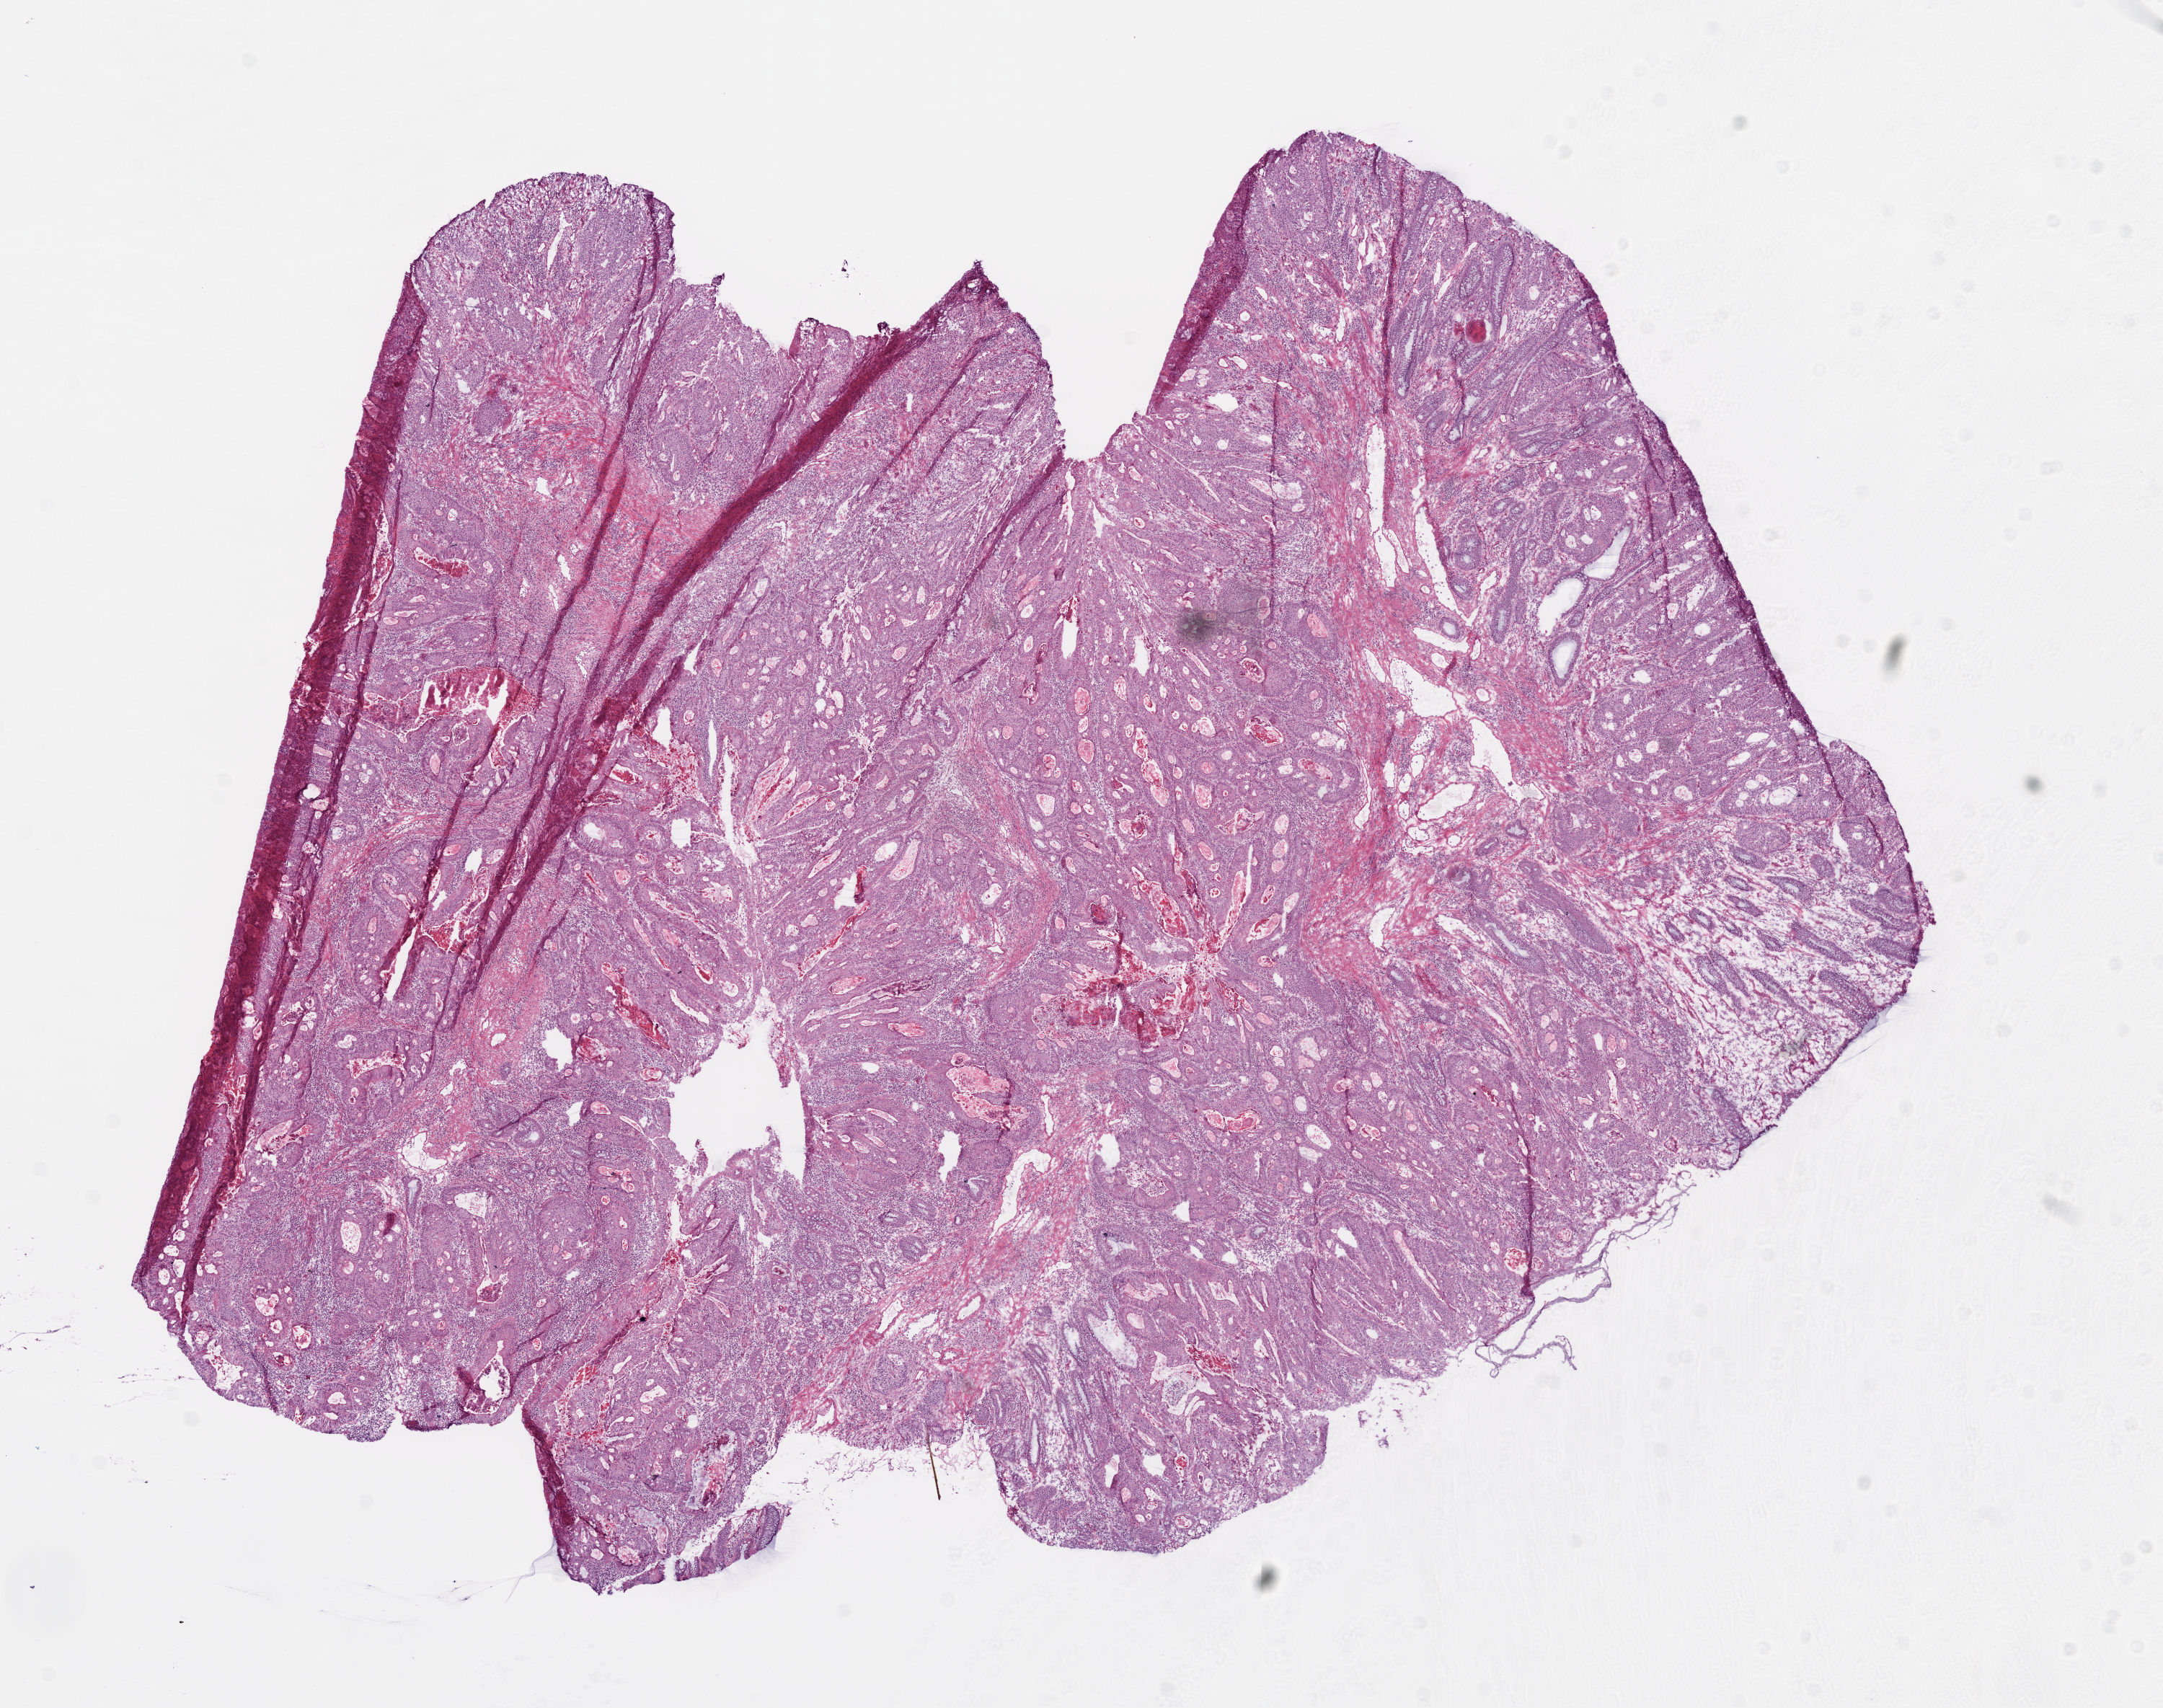
Whole-slide histology image, H&E, low-resolution overview of the scanned area, about 12.0 x 9.5 mm (slide scanned at 20x). Frozen section. Primary tumour sample from the colon. Male, age 74 years at initial diagnosis. Slide review estimates, as recorded: tumour cells 75%, tumour nuclei 85%, normal cells 5%, stromal cells 8%, necrosis 12%.
Lymph nodes positive (case pathology): 0 of 15 examined. AJCC pathologic stage: I. Pathologic diagnosis: Adenocarcinoma, NOS.